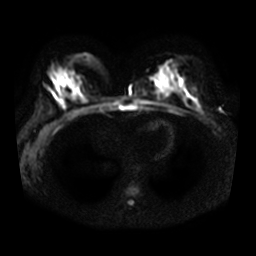
Breast MRI, one axial slice. Position 19 of 36 along the scan axis. Diffusion-weighted series; image 2 of 4 stored at this slice position (different b-values; order by instance number). 3 T. 256 × 256 image matrix, field of view 340 × 340 mm. Female patient.
Structures marked on this image (manually delineated by an expert):
- tumour on diffusion-weighted imaging: bounding box [x1, y1, x2, y2] px = [193, 106, 199, 111]